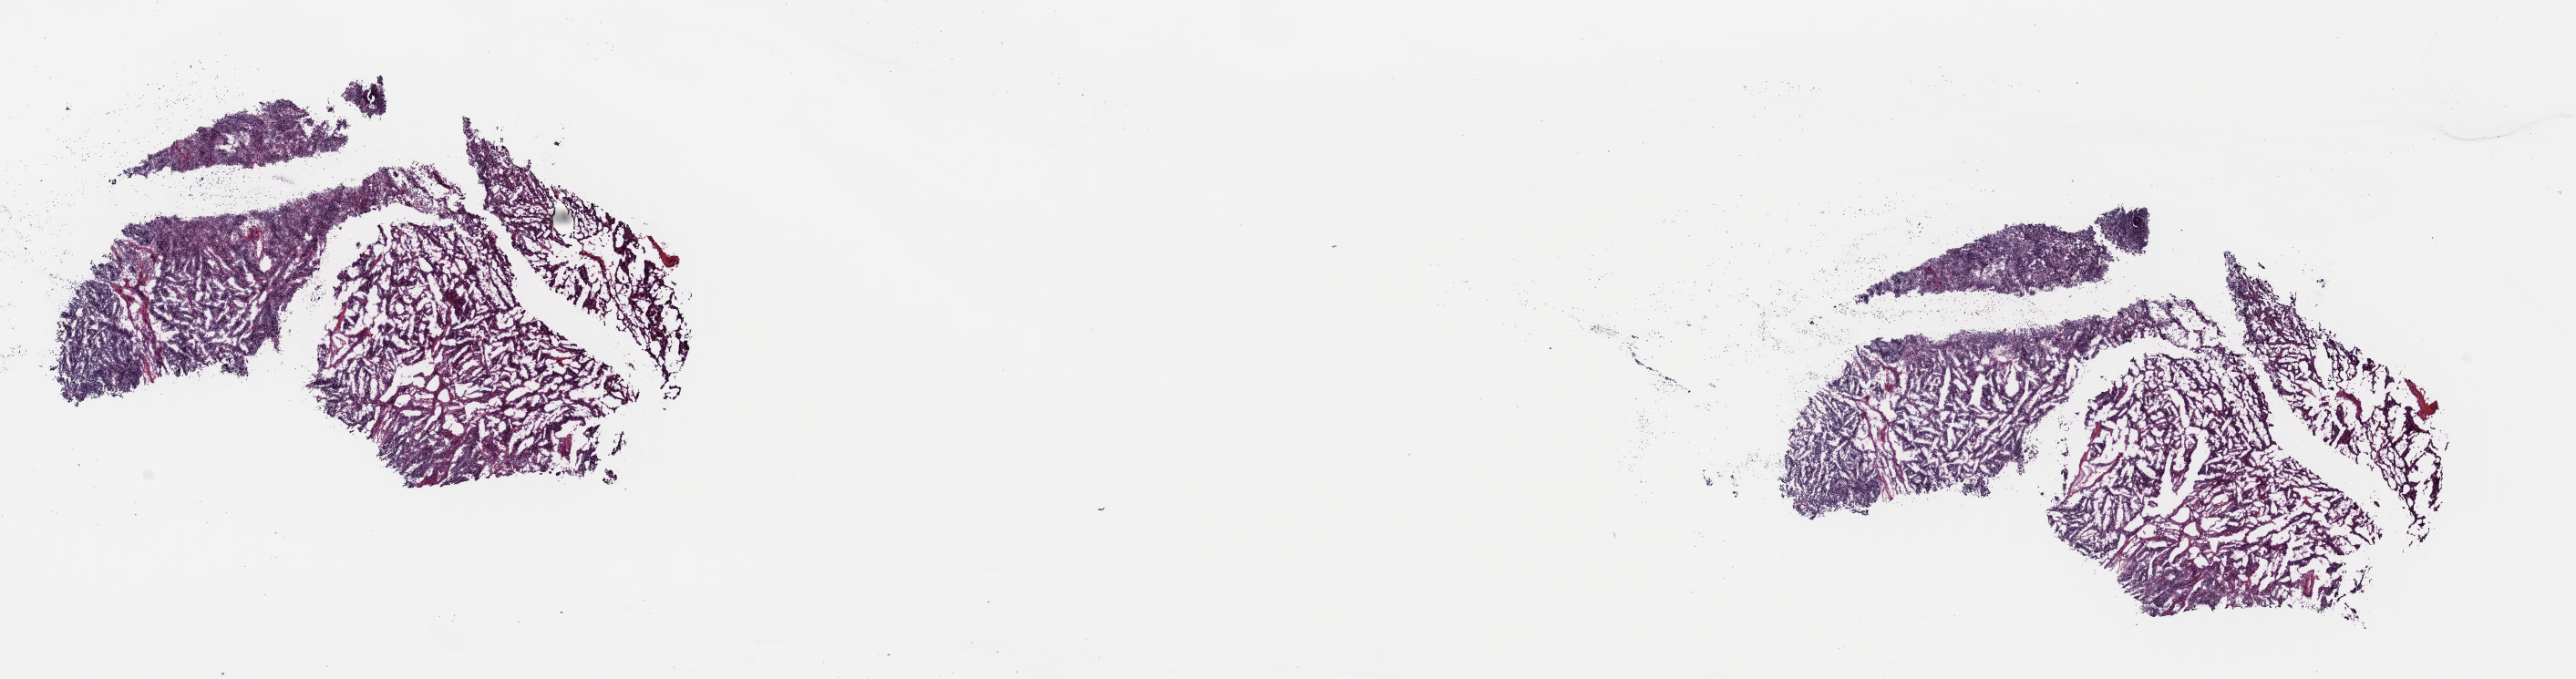
H&E-stained whole-slide image, shown as a low-resolution overview of the whole scanned area (about 22.2 x 5.9 mm). Frozen section from the top of the tissue portion. Metastatic tumour sample, sampled site: lymph nodes of inguinal region or leg. Female patient; age at initial diagnosis 74 years. Composition of this section per pathologist review: tumour cells 100%, tumour nuclei 80%, normal cells 0%, stromal cells 0%, necrosis 0%. Infiltration values recorded for this section: lymphocyte infiltration 3%, monocyte infiltration 0%, neutrophil infiltration 0%.
This section: metastatic tumour tissue. Patient diagnosis: Malignant melanoma, NOS.